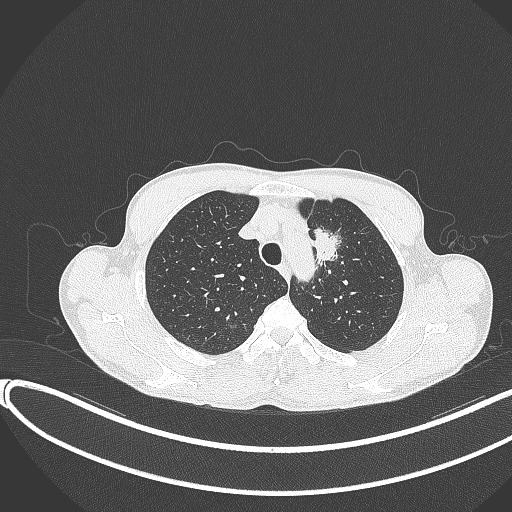
Chest CT, one axial slice; position 307 of 374 along the scan axis; reconstruction kernel B70f; 120 kVp; lung window (W 1500 / L -600 HU); 1 mm slice thickness; 512 × 512 image matrix, field of view 400 × 400 mm. Patient: male, 58 years. Case-level facts recorded for this patient, not image findings: clinical TNM (as recorded): T1c N1 M0.
Outlined on this slice (bounding box drawn by a radiologist):
- lung tumour (recorded histology: adenocarcinoma): bounding box [x1, y1, x2, y2] px = [310, 223, 351, 275]